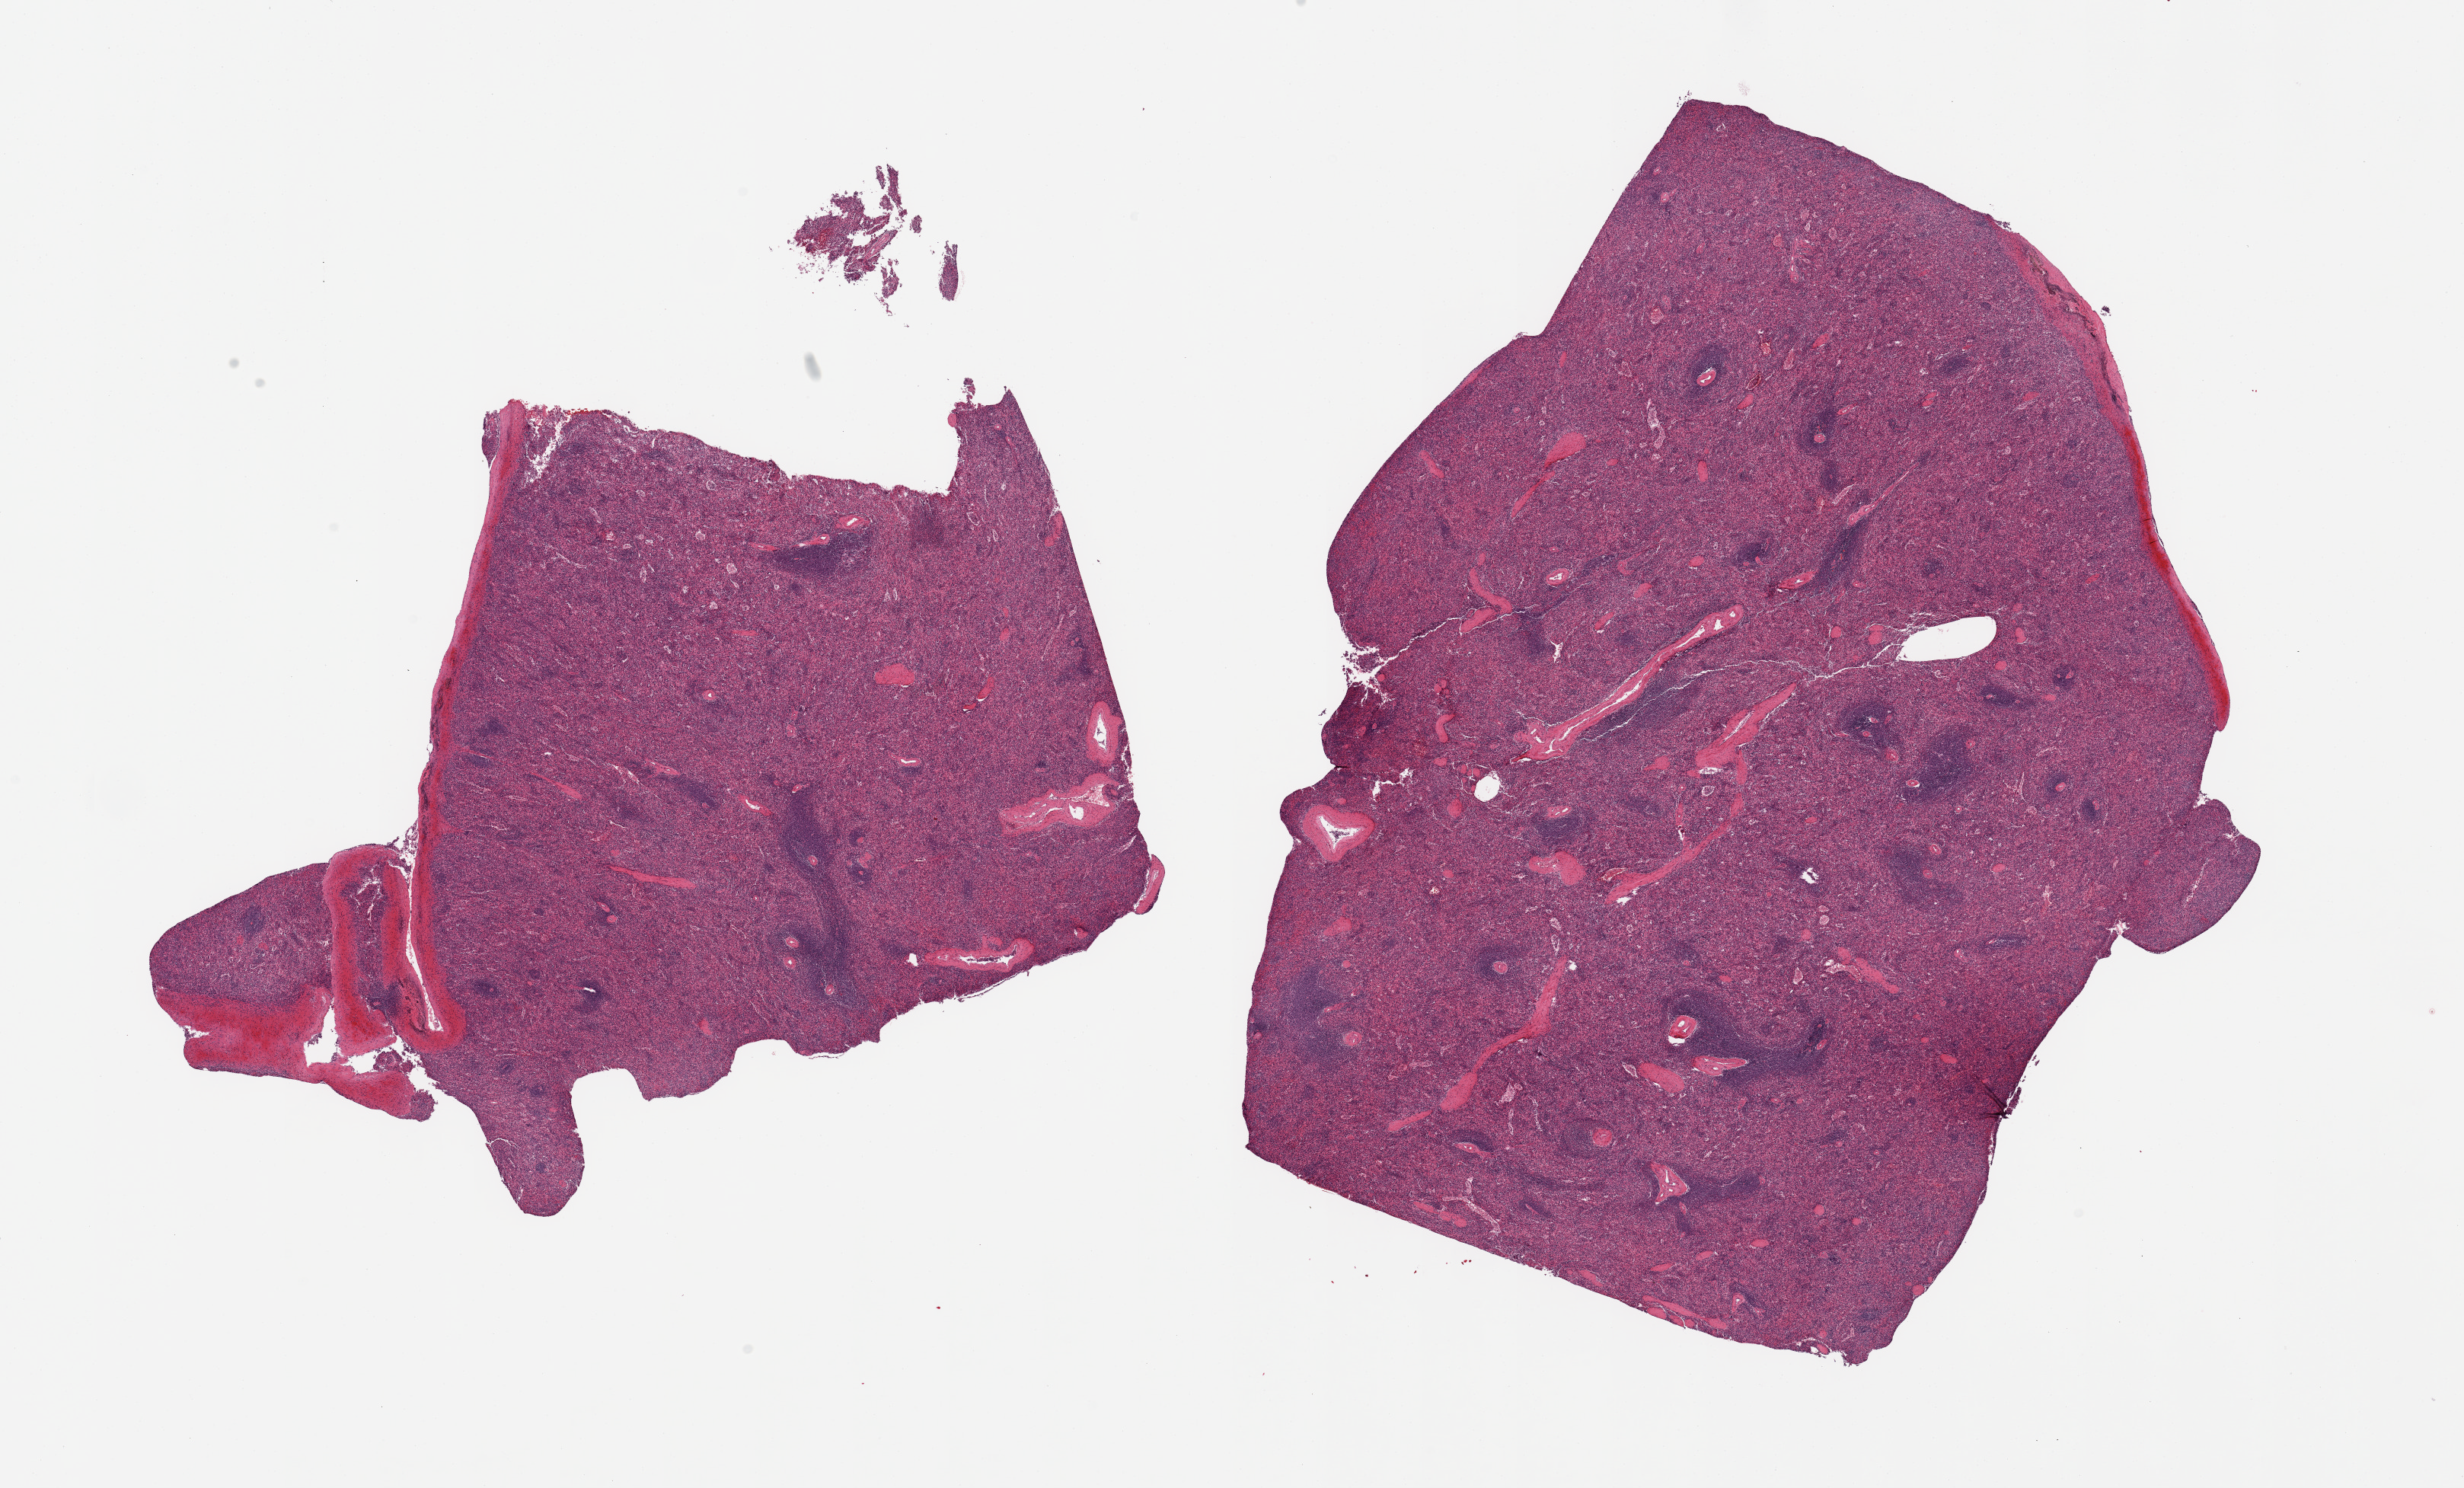
Whole-slide image, haematoxylin and eosin stain, whole scanned area (about 25.6 x 15.5 mm, from a 20x scan) shown as a low-resolution overview. PAXgene-fixed paraffin-embedded (PFPE) section. Sampled site (target tissue): spleen. Donor tissue sample. Donor: female.
Review note (as recorded): 2 pieces; contains 0.2 mm capsule on both pieces.